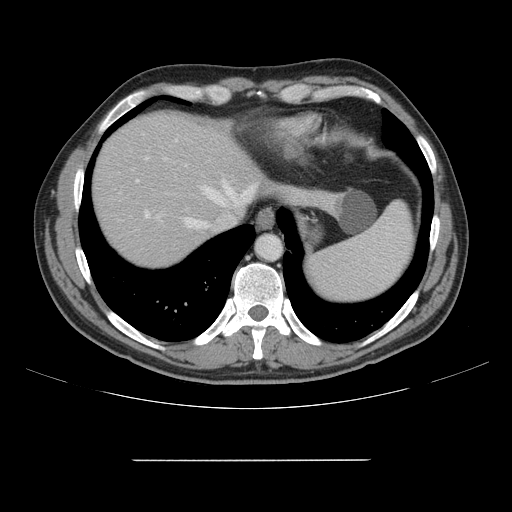
Contrast-enhanced abdominal CT, one axial slice; slice 132 of 164 in the series (ordered by position); intravenous contrast given; soft-tissue window (W 400 / L 40 HU); 2.5 mm slice thickness; 512 × 512 image matrix. Male patient, age 54 years. Case-level facts recorded for this patient, not image findings: diagnosis: colorectal cancer liver metastases, imaged before liver resection; multiple liver metastases: yes; largest metastasis: 1 cm; disease in both lobes: no.
Annotated regions visible in this slice (manually delineated by an expert):
- hepatic veins: bounding box <184,183,258,228> (left, top, right, bottom; pixels)
- liver: <93,113,326,269>
- planned liver remnant (the part of the liver to remain after resection): <93,113,250,269>
- portal vein (with intrahepatic branches): <133,139,217,218>